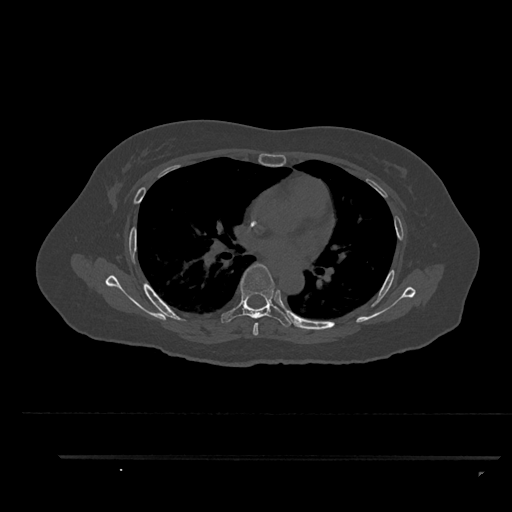
CT including the spine, one axial slice. Position 566 of 797 along the scan axis. Reconstruction kernel Br40s/3. Bone window (W 1800 / L 400 HU). 0.5 mm slice thickness. 512 × 512 image matrix, field of view 408 × 408 mm. Female patient, age 44 years. Case-level facts recorded for this patient, not image findings: primary cancer: renal; vertebrae with lytic lesions (as recorded): L1.
Structures marked on this image (semi-automatically segmented with operator editing):
- T5 vertebra: bounding box <253,322,258,336> (left, top, right, bottom; pixels)
- T6 vertebra: <221,263,294,327>